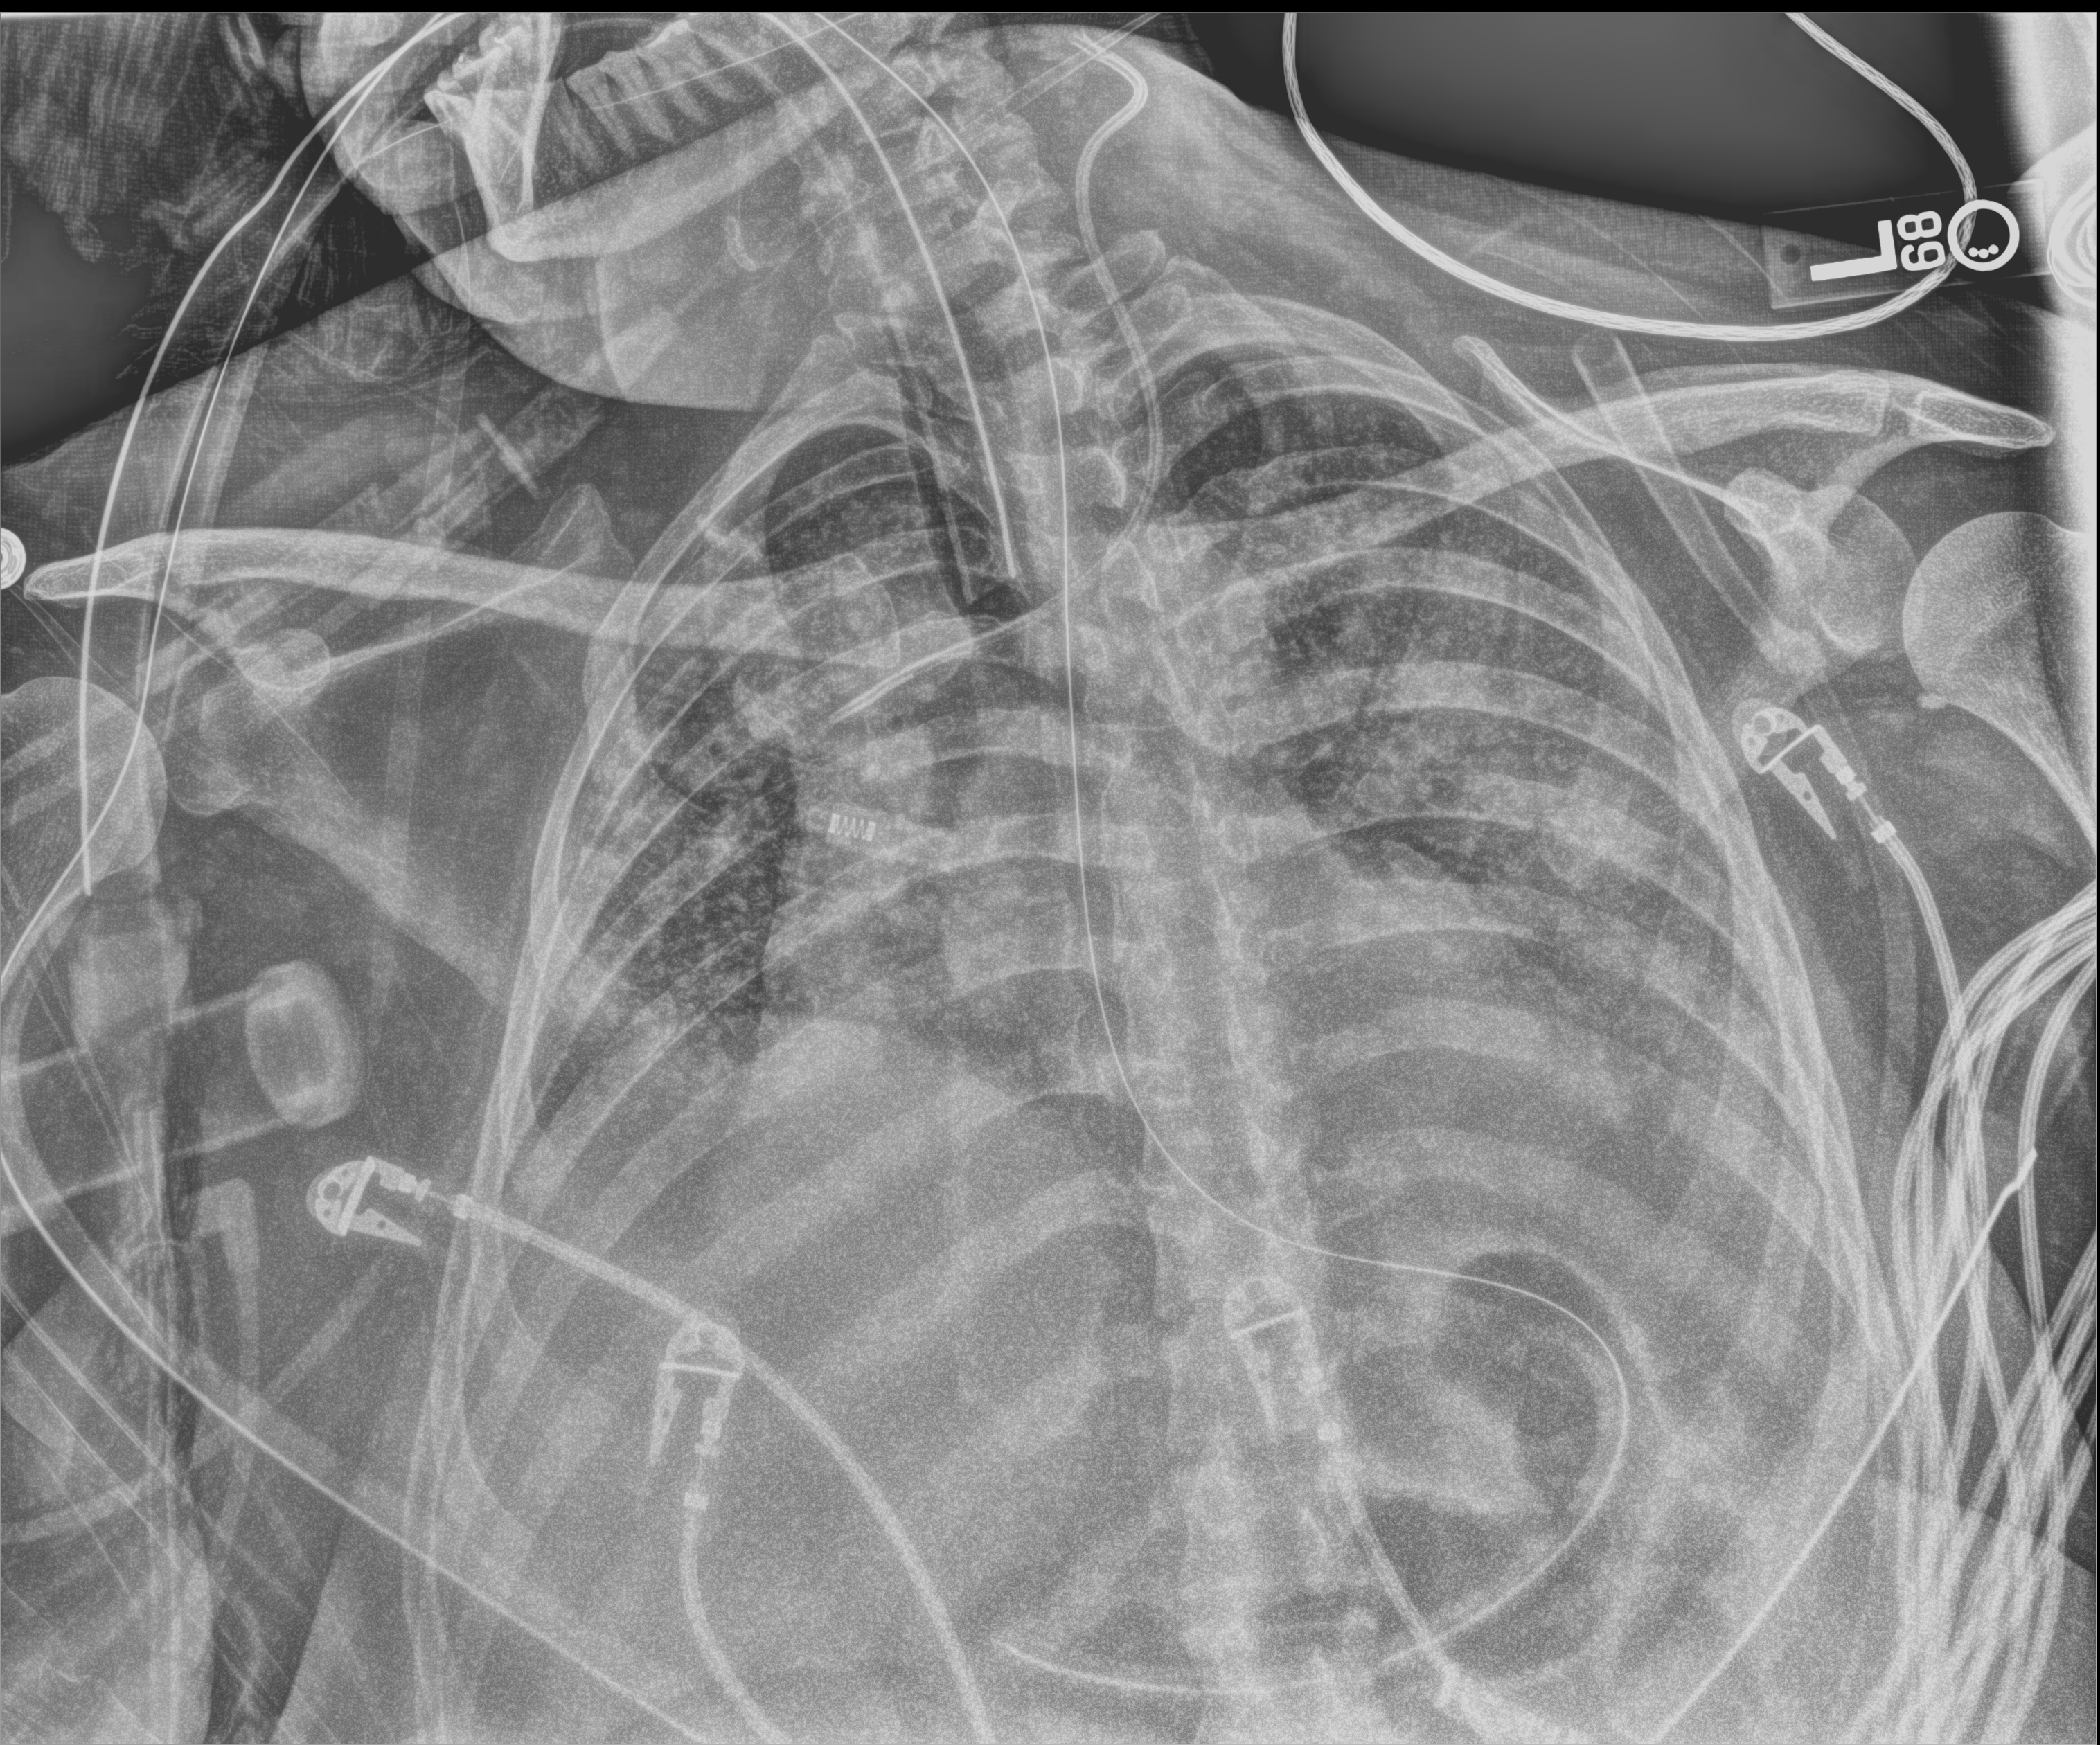
Chest radiograph (digital radiography); anteroposterior (AP) projection. Patient hospitalised with COVID-19; female, aged 18–59 years.
Hospital-stay facts (about this admission, not read from this image; timing relative to this image not recorded): mechanically ventilated during this hospital stay: yes; admitted to intensive care during this hospital stay: no.